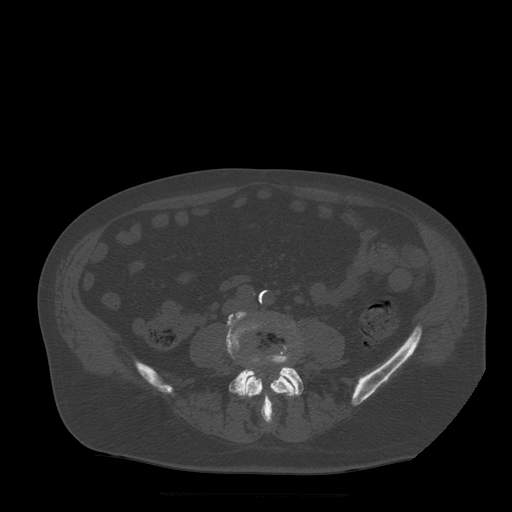
CT including the spine, one axial slice; slice 103 of 522 in the series (ordered by position); bone window (W 1800 / L 400 HU); 1.25 mm slice thickness; 512 × 512 image matrix. Patient age 72 years. From the clinical record (not read from this slice): primary cancer: prostate.
Outlined on this slice (semi-automatically segmented with operator editing):
- L4 vertebra: bounding box (x1, y1, x2, y2) in pixels: (226, 312, 297, 424)
- L5 vertebra: (229, 347, 304, 416)